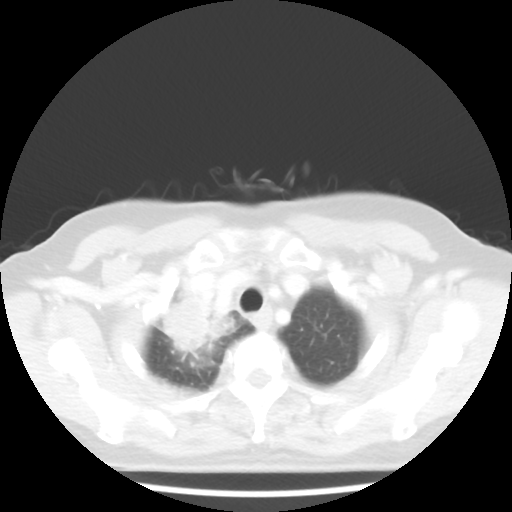
Chest CT, one axial slice; reconstruction kernel STANDARD; 100 kVp; lung window (W 1500 / L -600 HU); 5 mm slice thickness; 512 × 512 image matrix. Patient: female, 62 years. Case-level facts recorded for this patient, not image findings: clinical TNM (as recorded): T3 N0 M0; histopathological grade: G3.
Outlined on this slice (rectangle marked by the reading radiologist):
- lung tumour (recorded histology: small cell carcinoma): box from (x=151, y=286) to (x=220, y=361) px